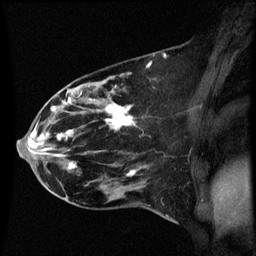
Breast MRI (dynamic contrast-enhanced), one sagittal slice. Slice 26 of 60 in the series (ordered by position). Dynamic contrast-enhanced series, image 2 of 3 at this slice position (ordered by acquisition). 1.5 T. TE 4.2 ms, TR 8.9 ms. 2 mm slice thickness. 256 × 256 image matrix, field of view 200 × 200 mm. Patient: female, 44 years. From the clinical record (not read from this slice): setting: breast cancer imaged before/during neoadjuvant chemotherapy; receptor status: HR-positive, HER2-negative.
Outlined on this slice (semi-automatic segmentation, software-assisted and operator-edited):
- analysis volume of interest (the breast-tissue region the enhancement analysis was run in; not a lesion): bounding box <43,78,150,189> (left, top, right, bottom; pixels)
- tumour enhancement mask (voxels above the 70 % enhancement threshold inside the analysis volume of interest): <56,98,135,177>